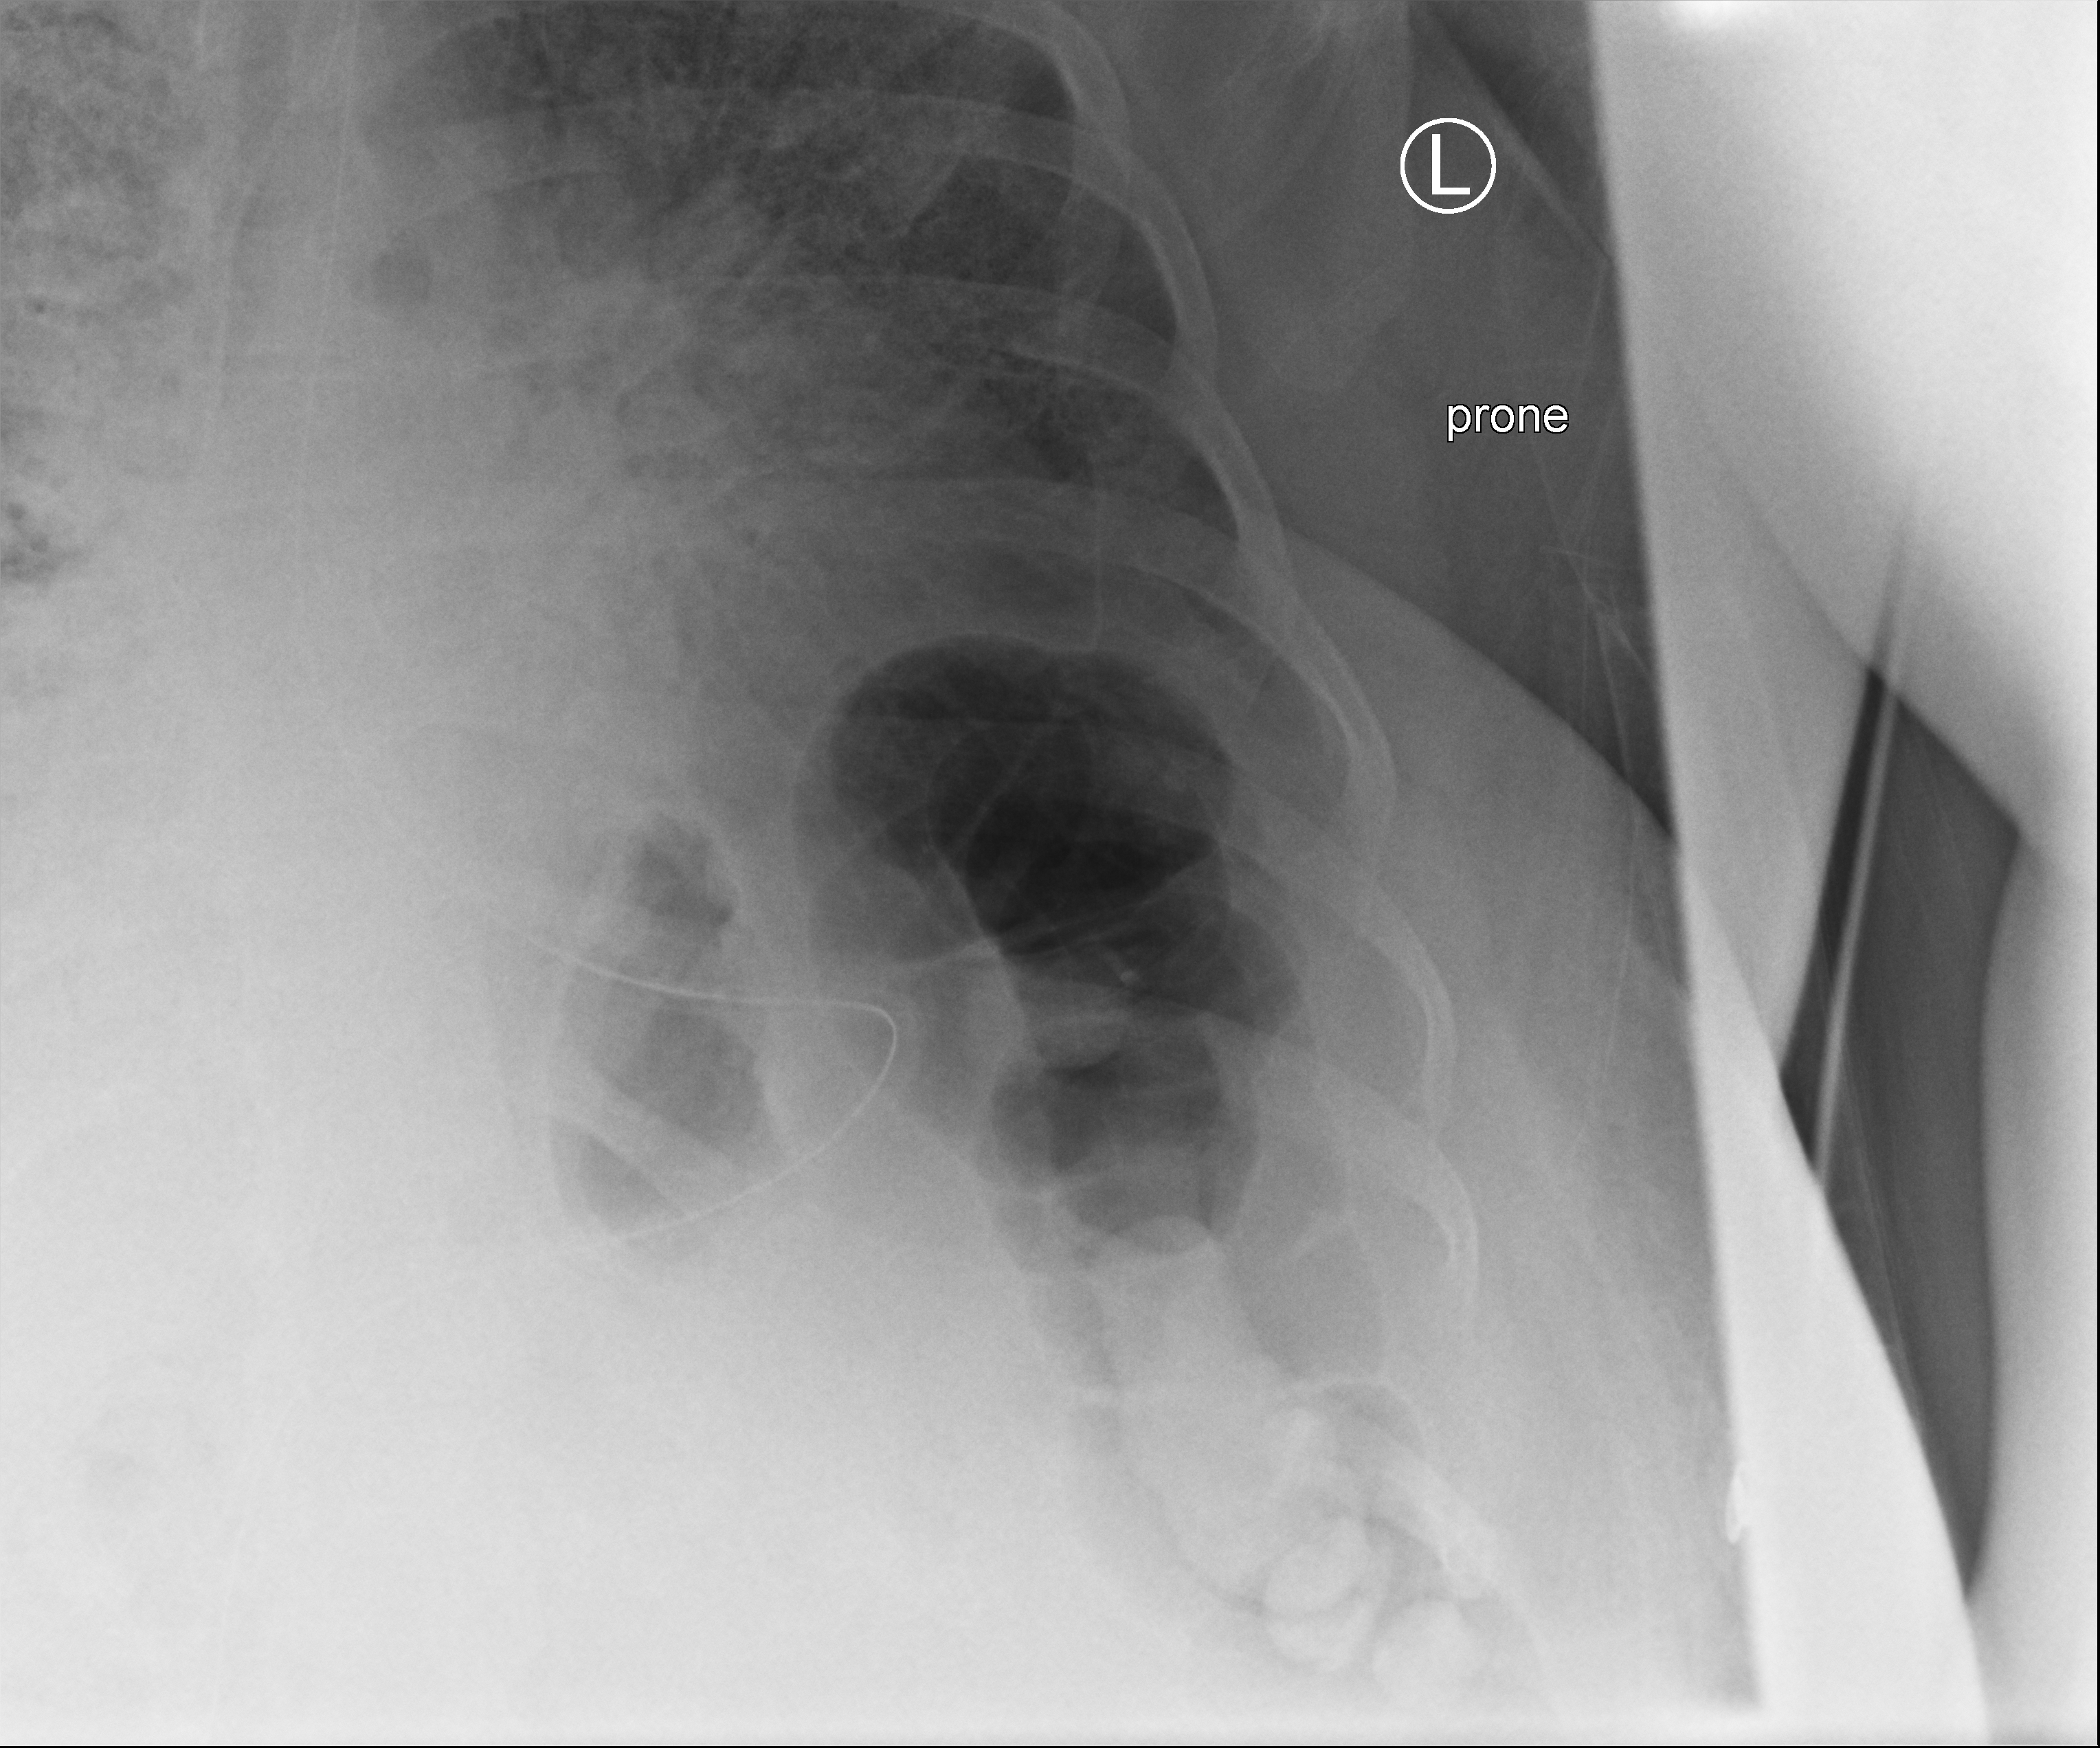
Bedside chest radiograph (computed radiography), anteroposterior (AP) projection. Patient hospitalised with COVID-19, aged 18–59 years.
Hospital-stay facts (about this admission, not read from this image; timing relative to this image not recorded):
- hypertension (admission record): no
- length of hospital stay: 16 days